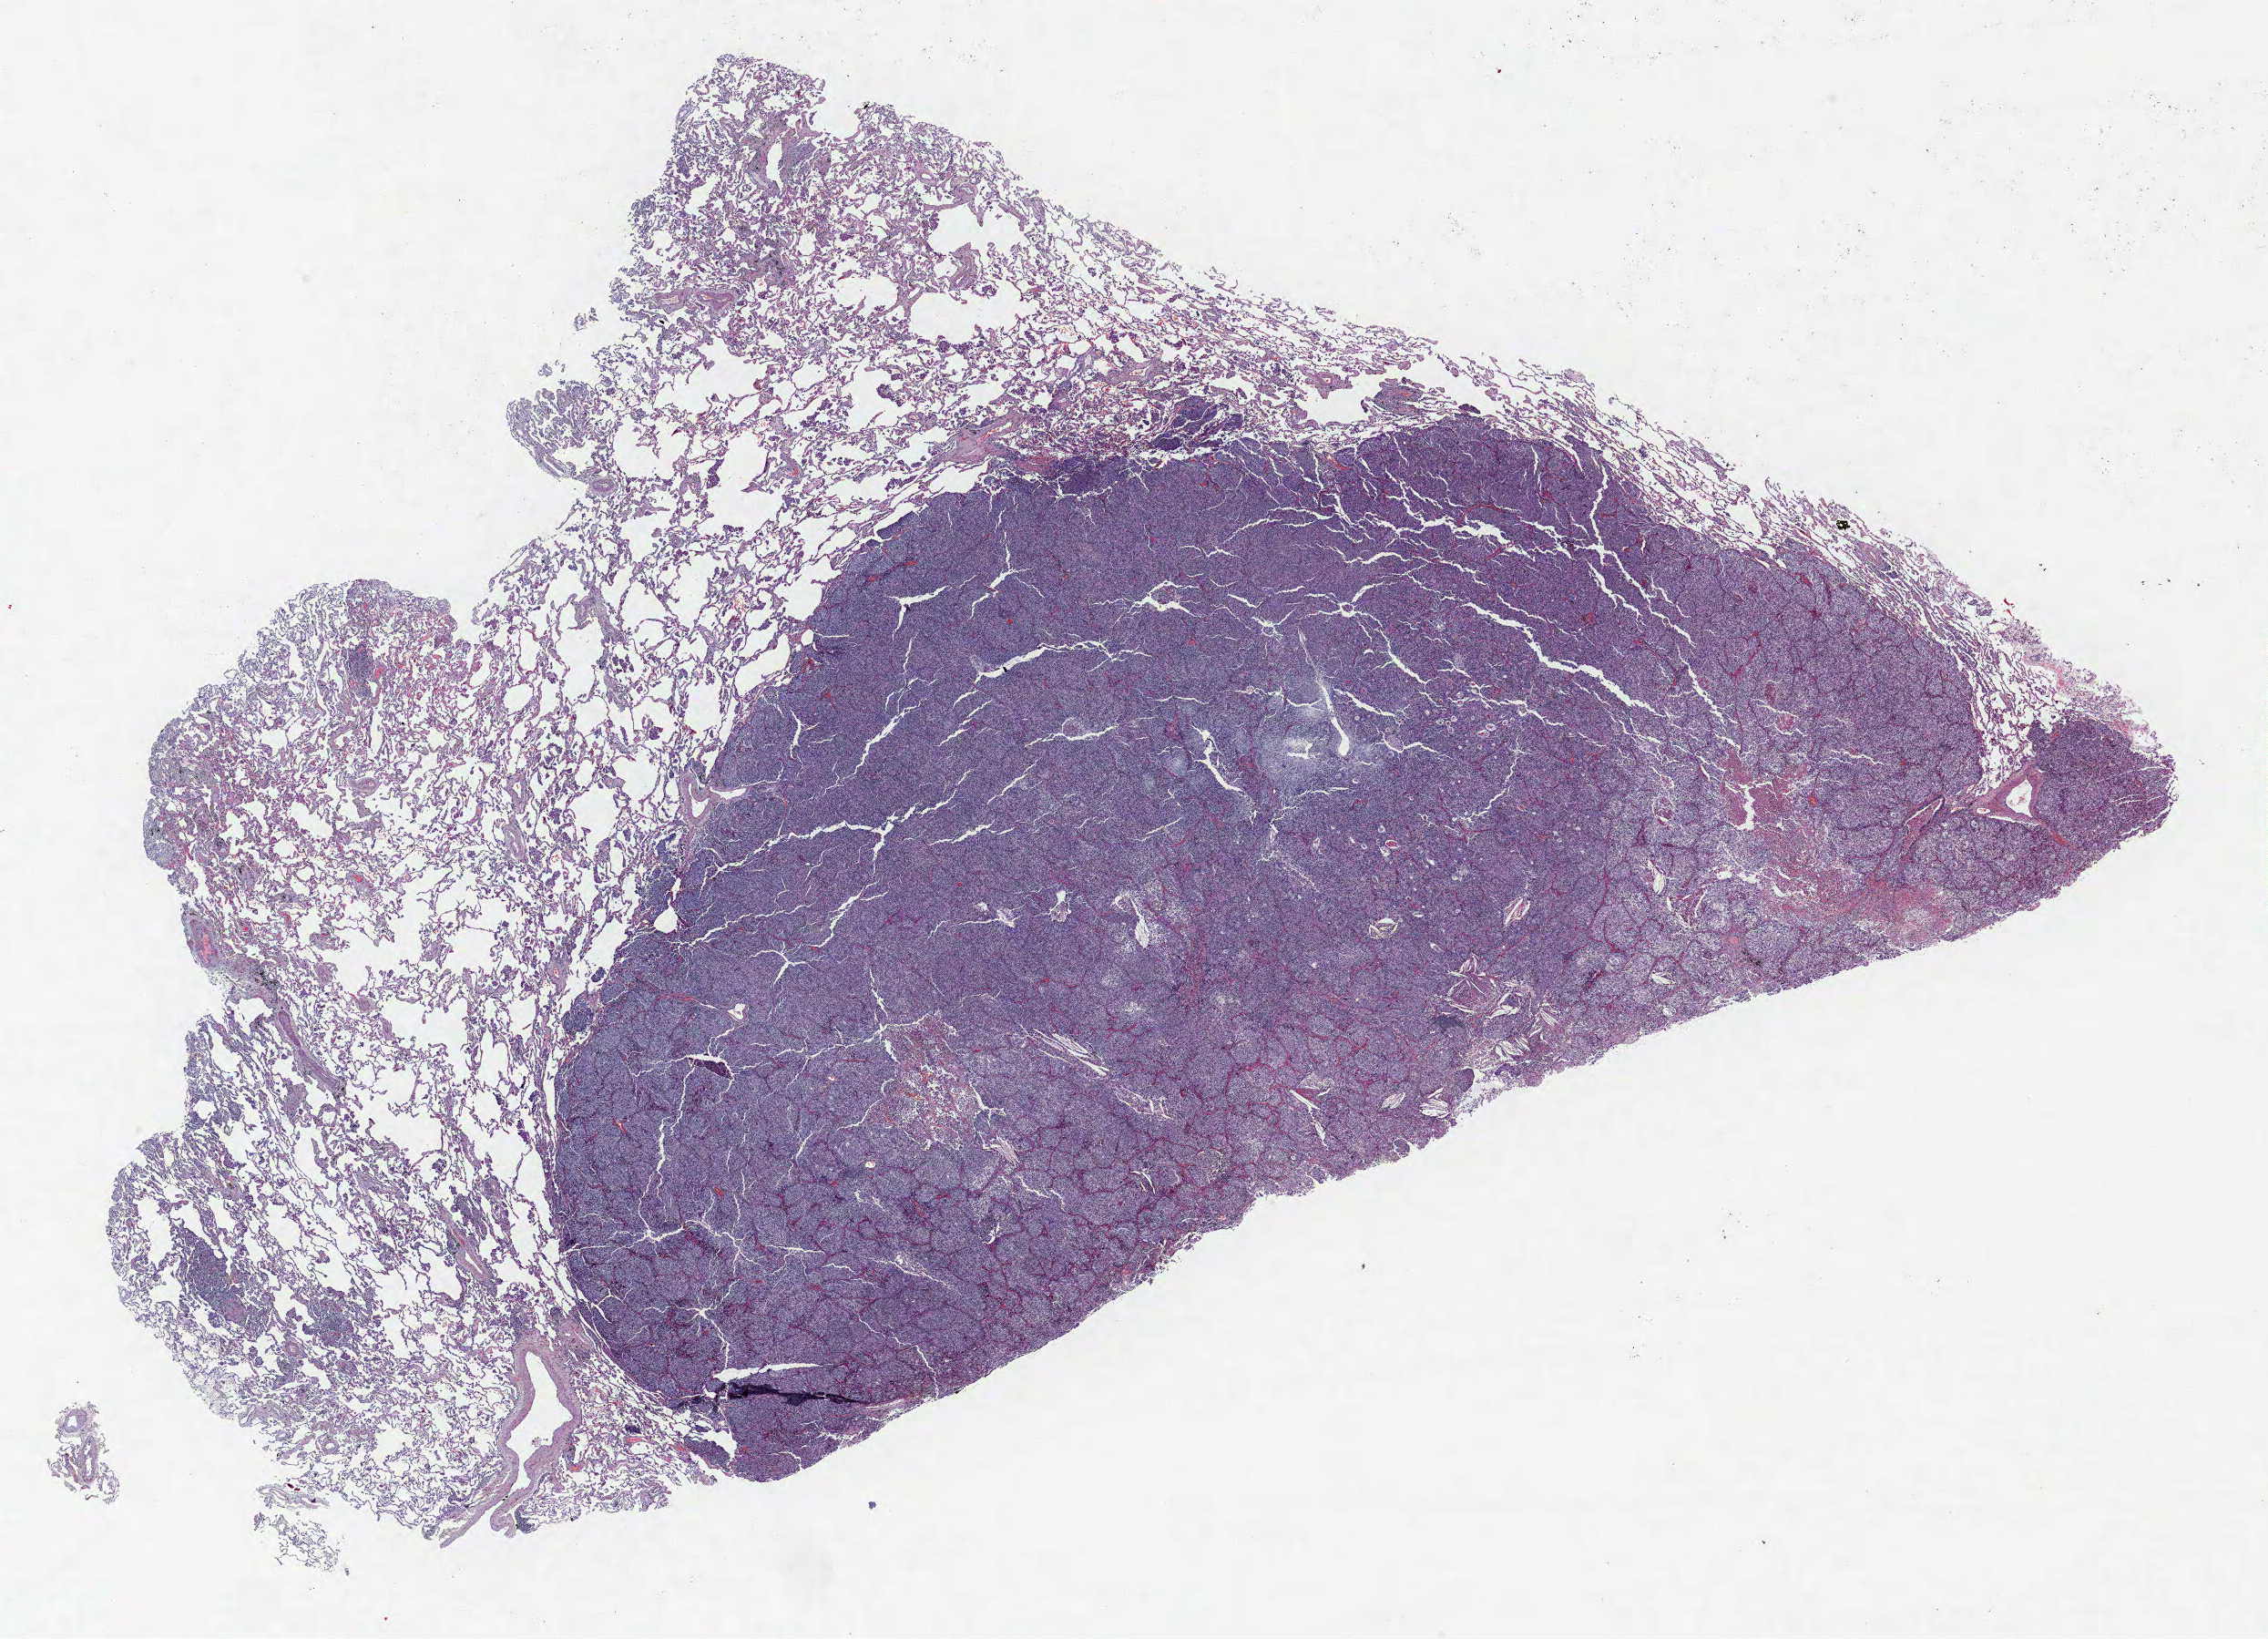
H&E-stained whole-slide image, shown as a low-resolution overview of the whole scanned area (about 19.9 x 14.4 mm, slide scanned at 40x); formalin-fixed paraffin-embedded (FFPE) section; lung tissue. Male patient, aged 65 at enrolment. Former smoker at enrolment. Grade: poorly differentiated (G3).
- primary tumour location (clinical record): right upper lobe
- ICD-O-3 topography: upper lobe of lung (C34.1)
- participant's lung-cancer diagnosis: Adenocarcinoma, NOS (ICD-O-3 8140/3)
- stage (AJCC 6th edition): IA
- tumour size (pathology): 17 mm